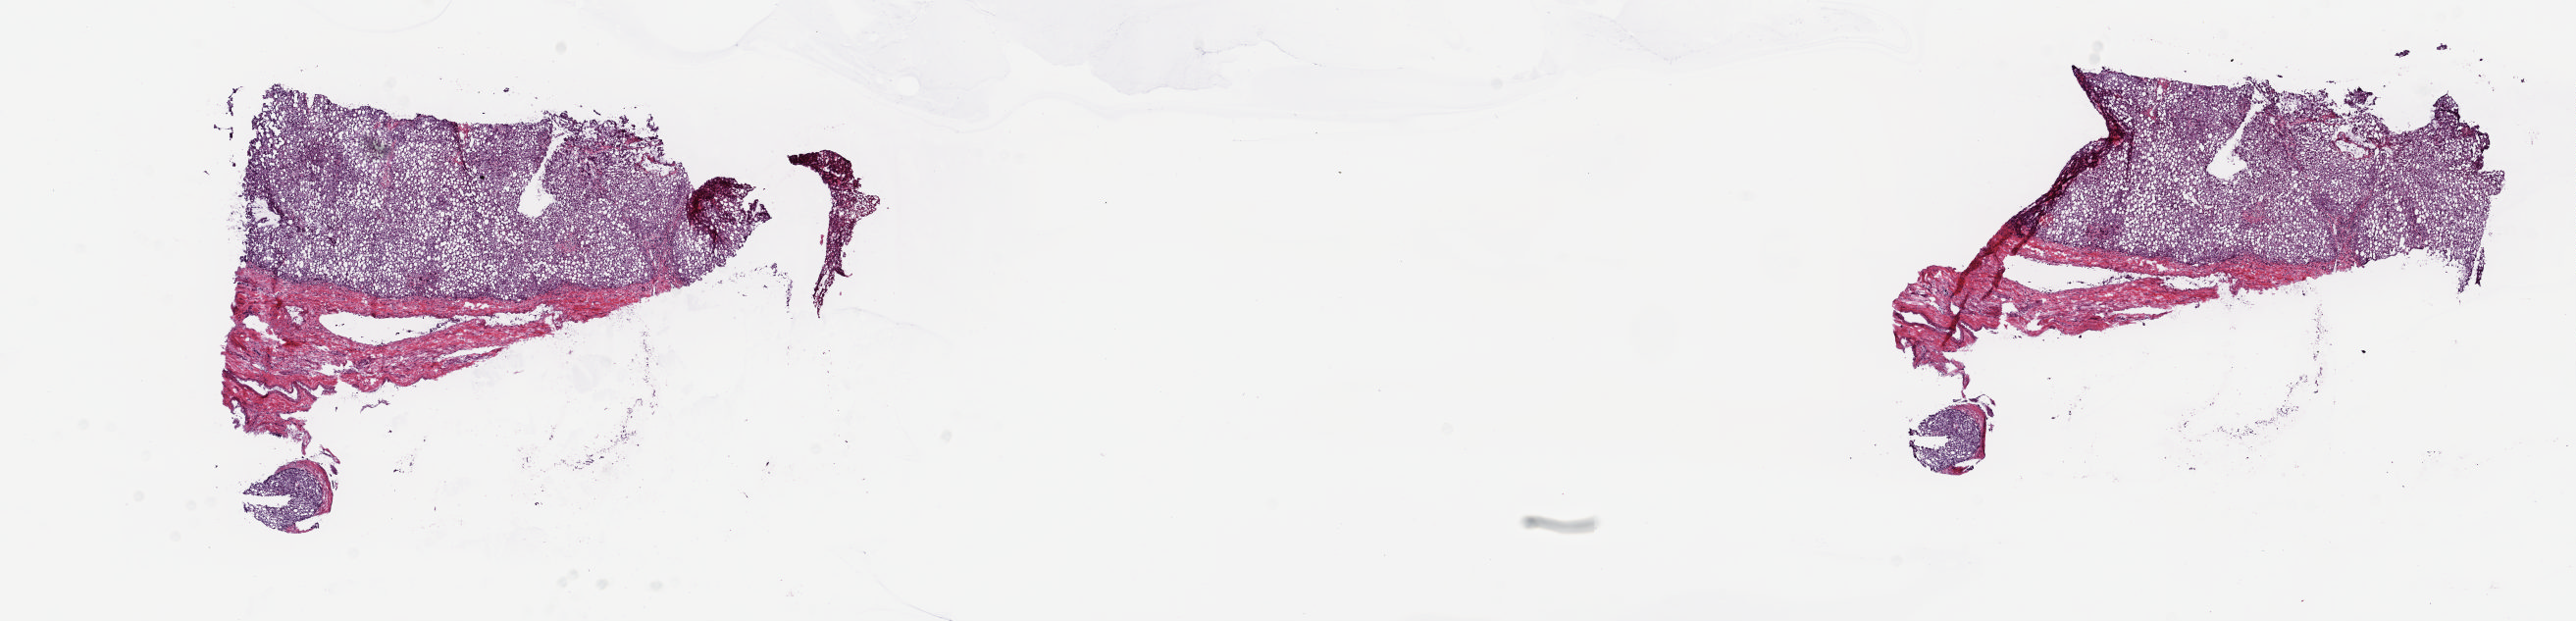
Digitized Hematoxylin and eosin (H&E) stained tissue section (whole slide), a low-resolution overview of the entire scanned area, about 20.8 x 5.0 mm, frozen section, liver, solid tissue normal (non-tumour tissue) sample. Male, age 76 years at initial diagnosis. Pathologist review of this section (percent, as recorded): tumour cells 0%, tumour nuclei 0%, normal cells 70%, stromal cells 30%, necrosis 0%. Infiltration values recorded for this section: lymphocyte infiltration 10%, monocyte infiltration 0%, neutrophil infiltration 0%.
This section: solid tissue normal (non-tumour) sample from the same patient. Patient diagnosis: Hepatocellular carcinoma, NOS.